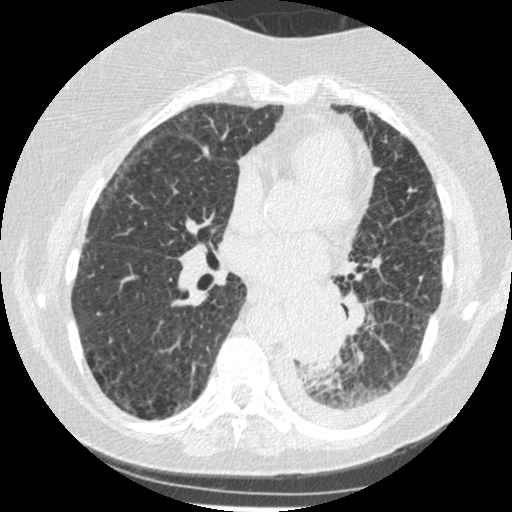
Low-dose screening chest CT, axial slice. Third annual screen. Lung window (W 1500 / L -600 HU). 1.25 mm slice thickness. Standard (soft-tissue) reconstruction kernel (STANDARD). Slice 227 of 341 in the series. Female, age 60 years at enrolment. Former smoker at enrolment.
• Expert reader's lesion annotation, bounding box <274,304,342,375> (left, top, right, bottom; pixels).
• Reader record for this screening exam (exam-level; its link to the box is not recorded): non-calcified nodule or mass ≥4 mm, left lower lobe, 54 × 38 mm, smooth margins, soft tissue attenuation, pre-existing on the prior screen: yes; interval growth: yes.
• Lung cancer was diagnosed 15 days after this screen: small cell carcinoma, NOS, left lower lobe, undifferentiated (G4), stage IV (AJCC 6th edition), 69 mm at pathology.